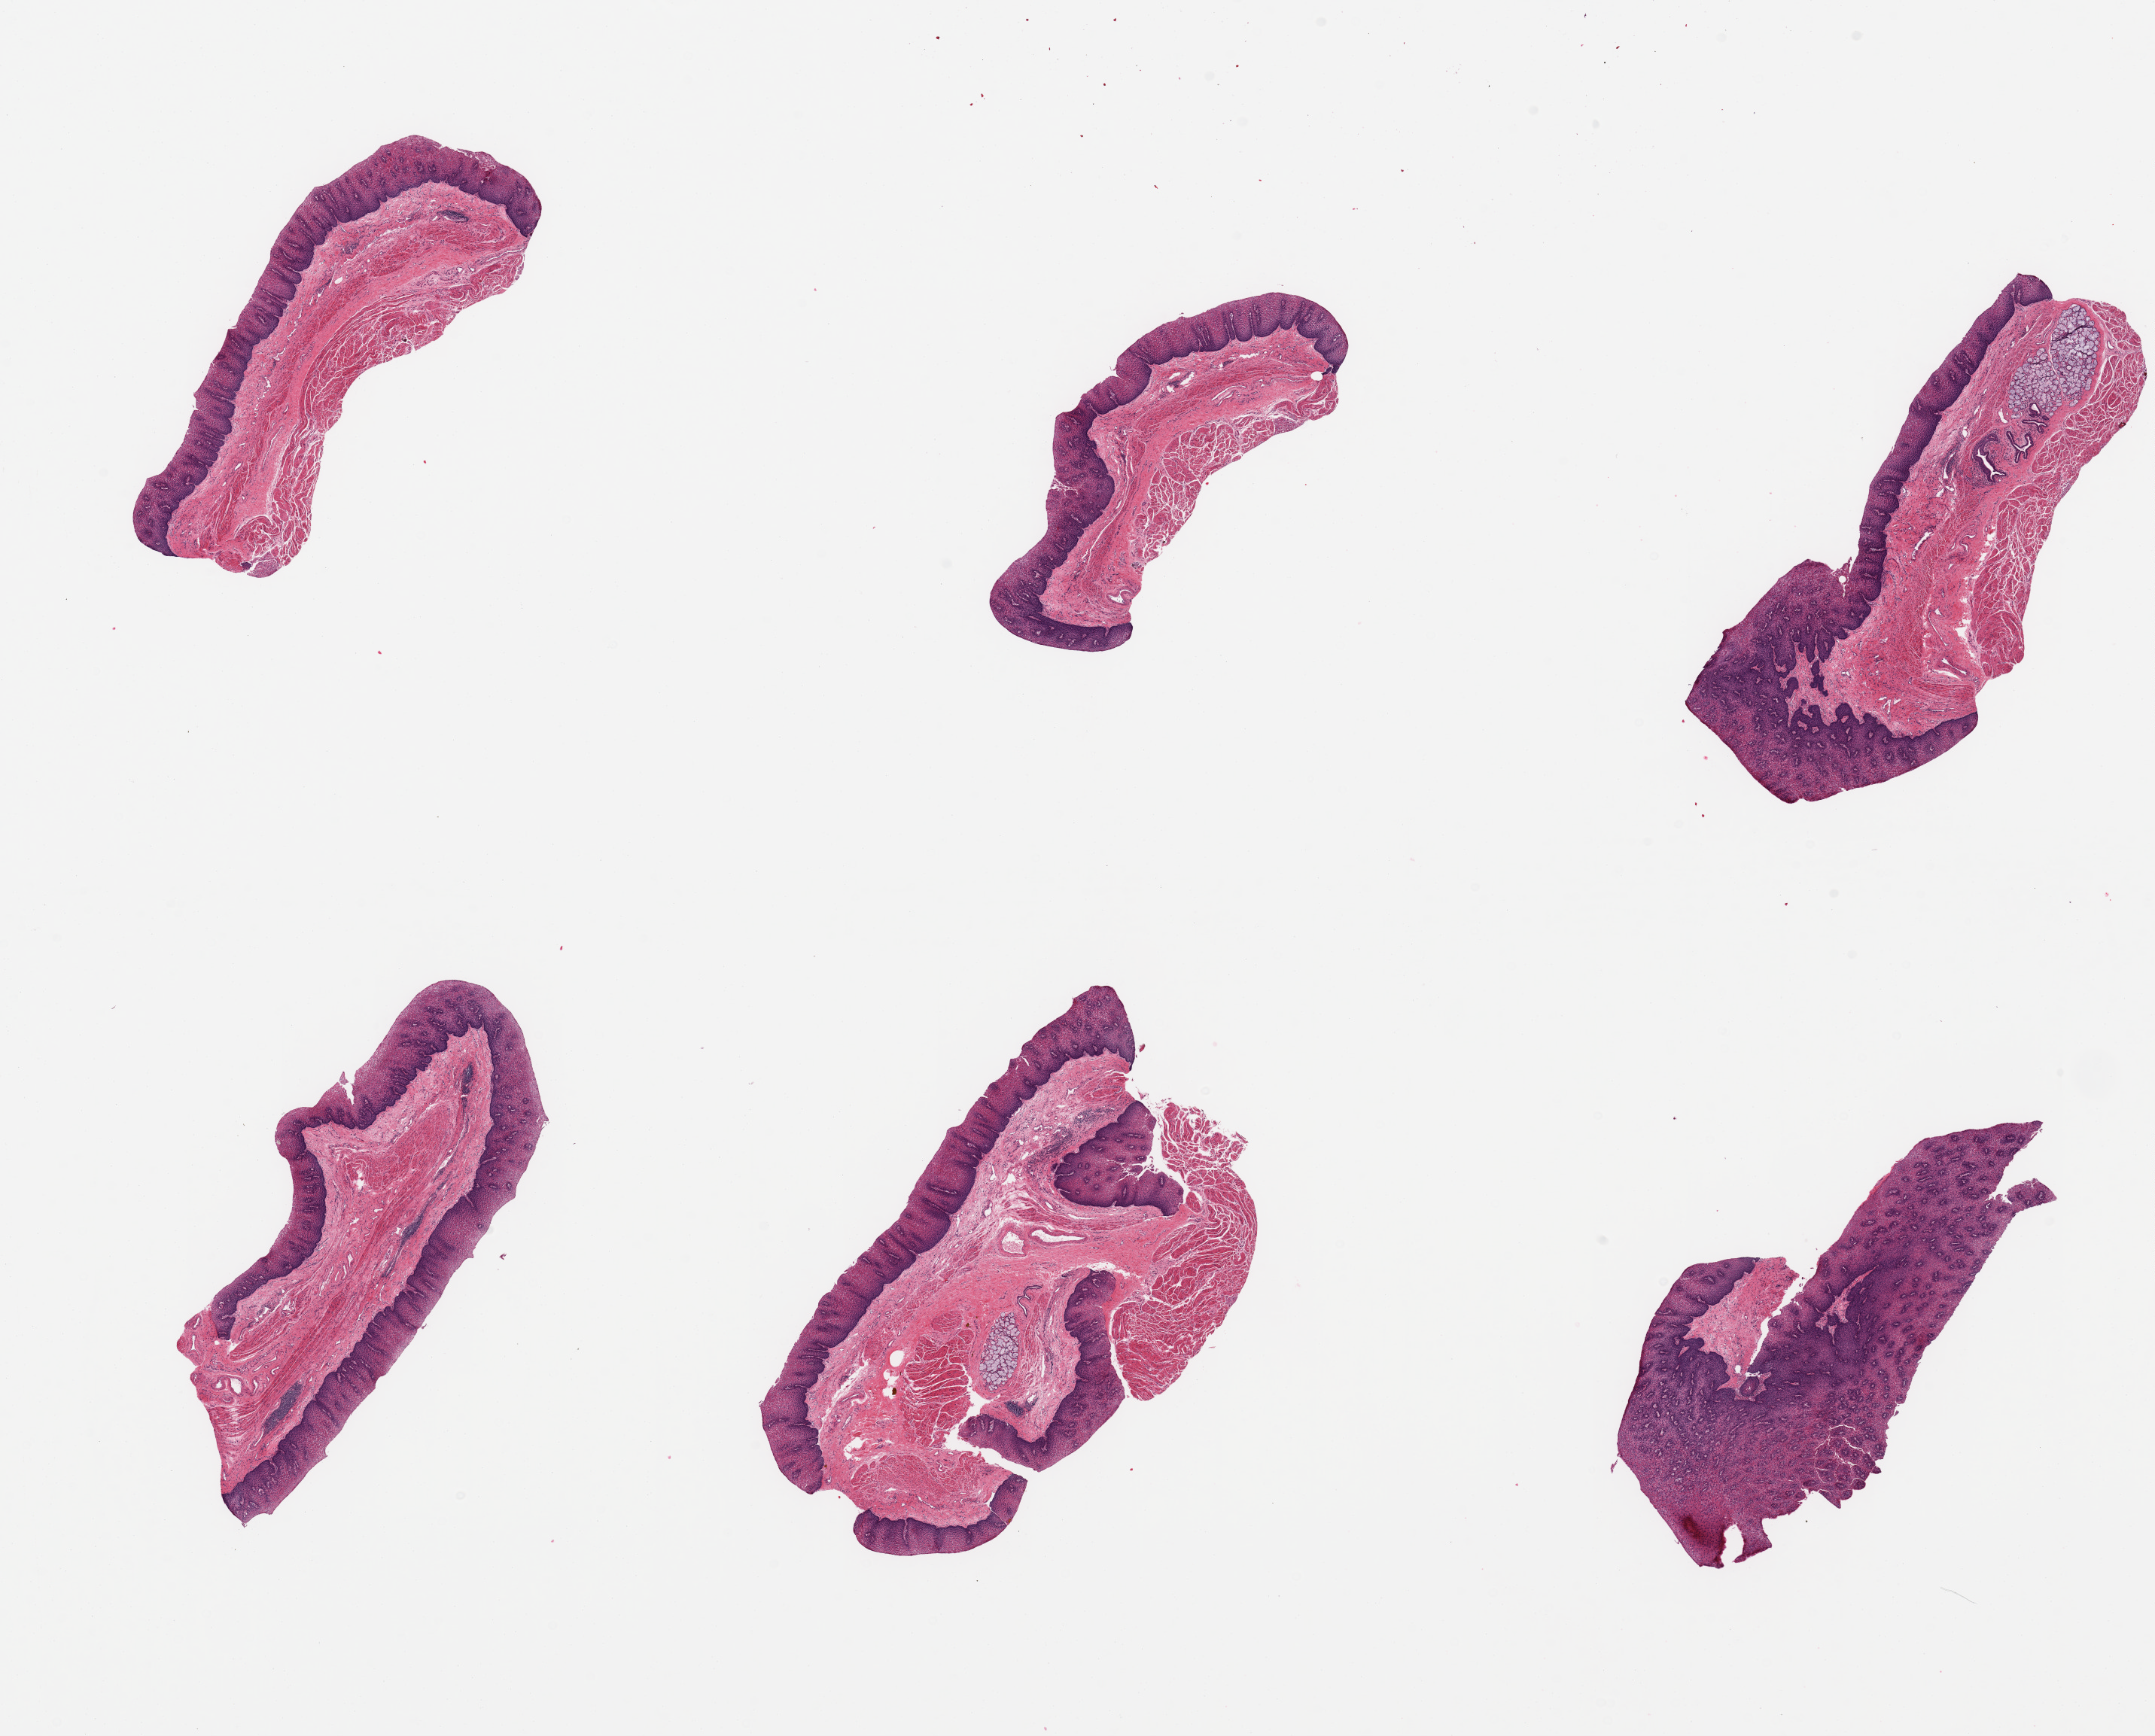
Digitized hematoxylin and eosin (H&E)-stained section, brightfield — a low-resolution overview of the entire scanned area, about 22.6 x 18.2 mm (acquisition: 20x scan). PAXgene-fixed paraffin-embedded (PFPE) section. Target tissue: esophageal mucous membrane. Tissue donor sample. Donor sex: male.
Pathologist's review note for this sample: 2 pieces; muscularis propria makes up 20 to 30% in 4 of 6 pieces; large submucosal gland comprises 10% of 1 piece, 5% of another piece.